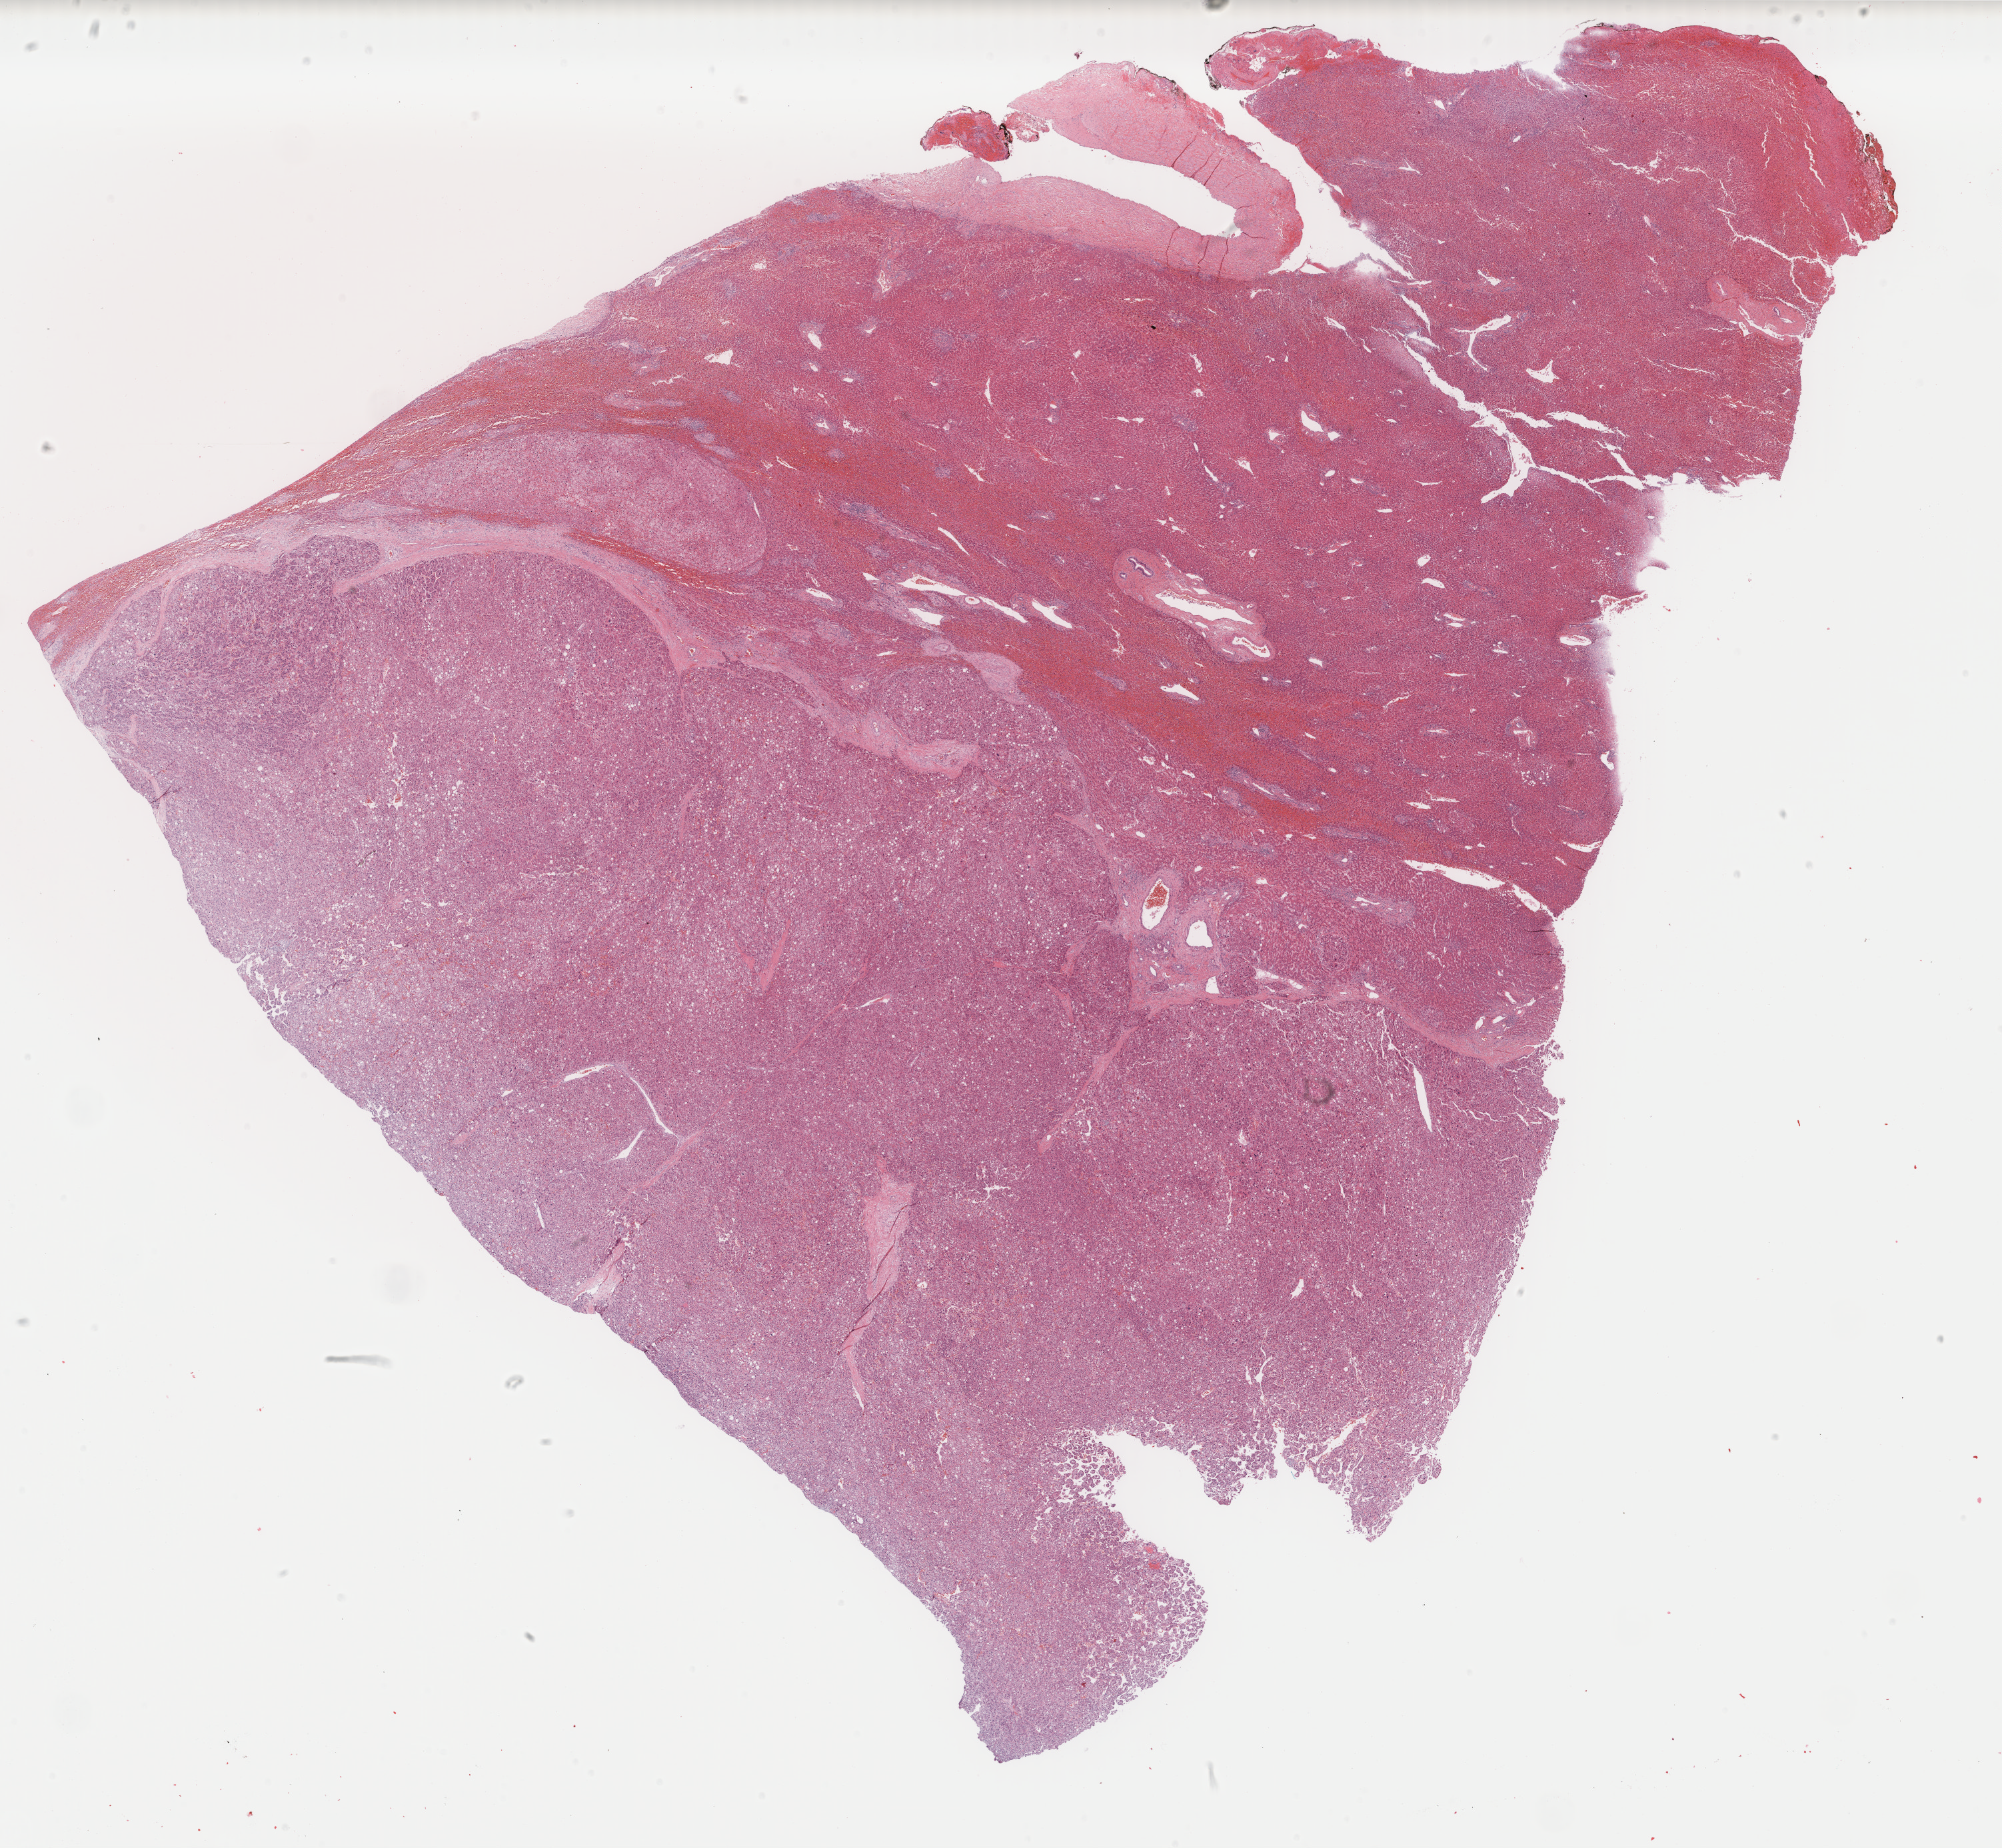
Digitized Hematoxylin and eosin (H&E) stained tissue section (whole slide) — whole scanned area (about 23.8 x 22.0 mm) shown as a low-resolution overview. Formalin-fixed paraffin-embedded (FFPE) diagnostic section. Primary tumour sample from the liver. Patient: male, age at initial diagnosis 71 years. Histologic grade: G1 (well differentiated).
Diagnosis: Hepatocellular carcinoma, NOS. AJCC pathologic stage: IIIA.